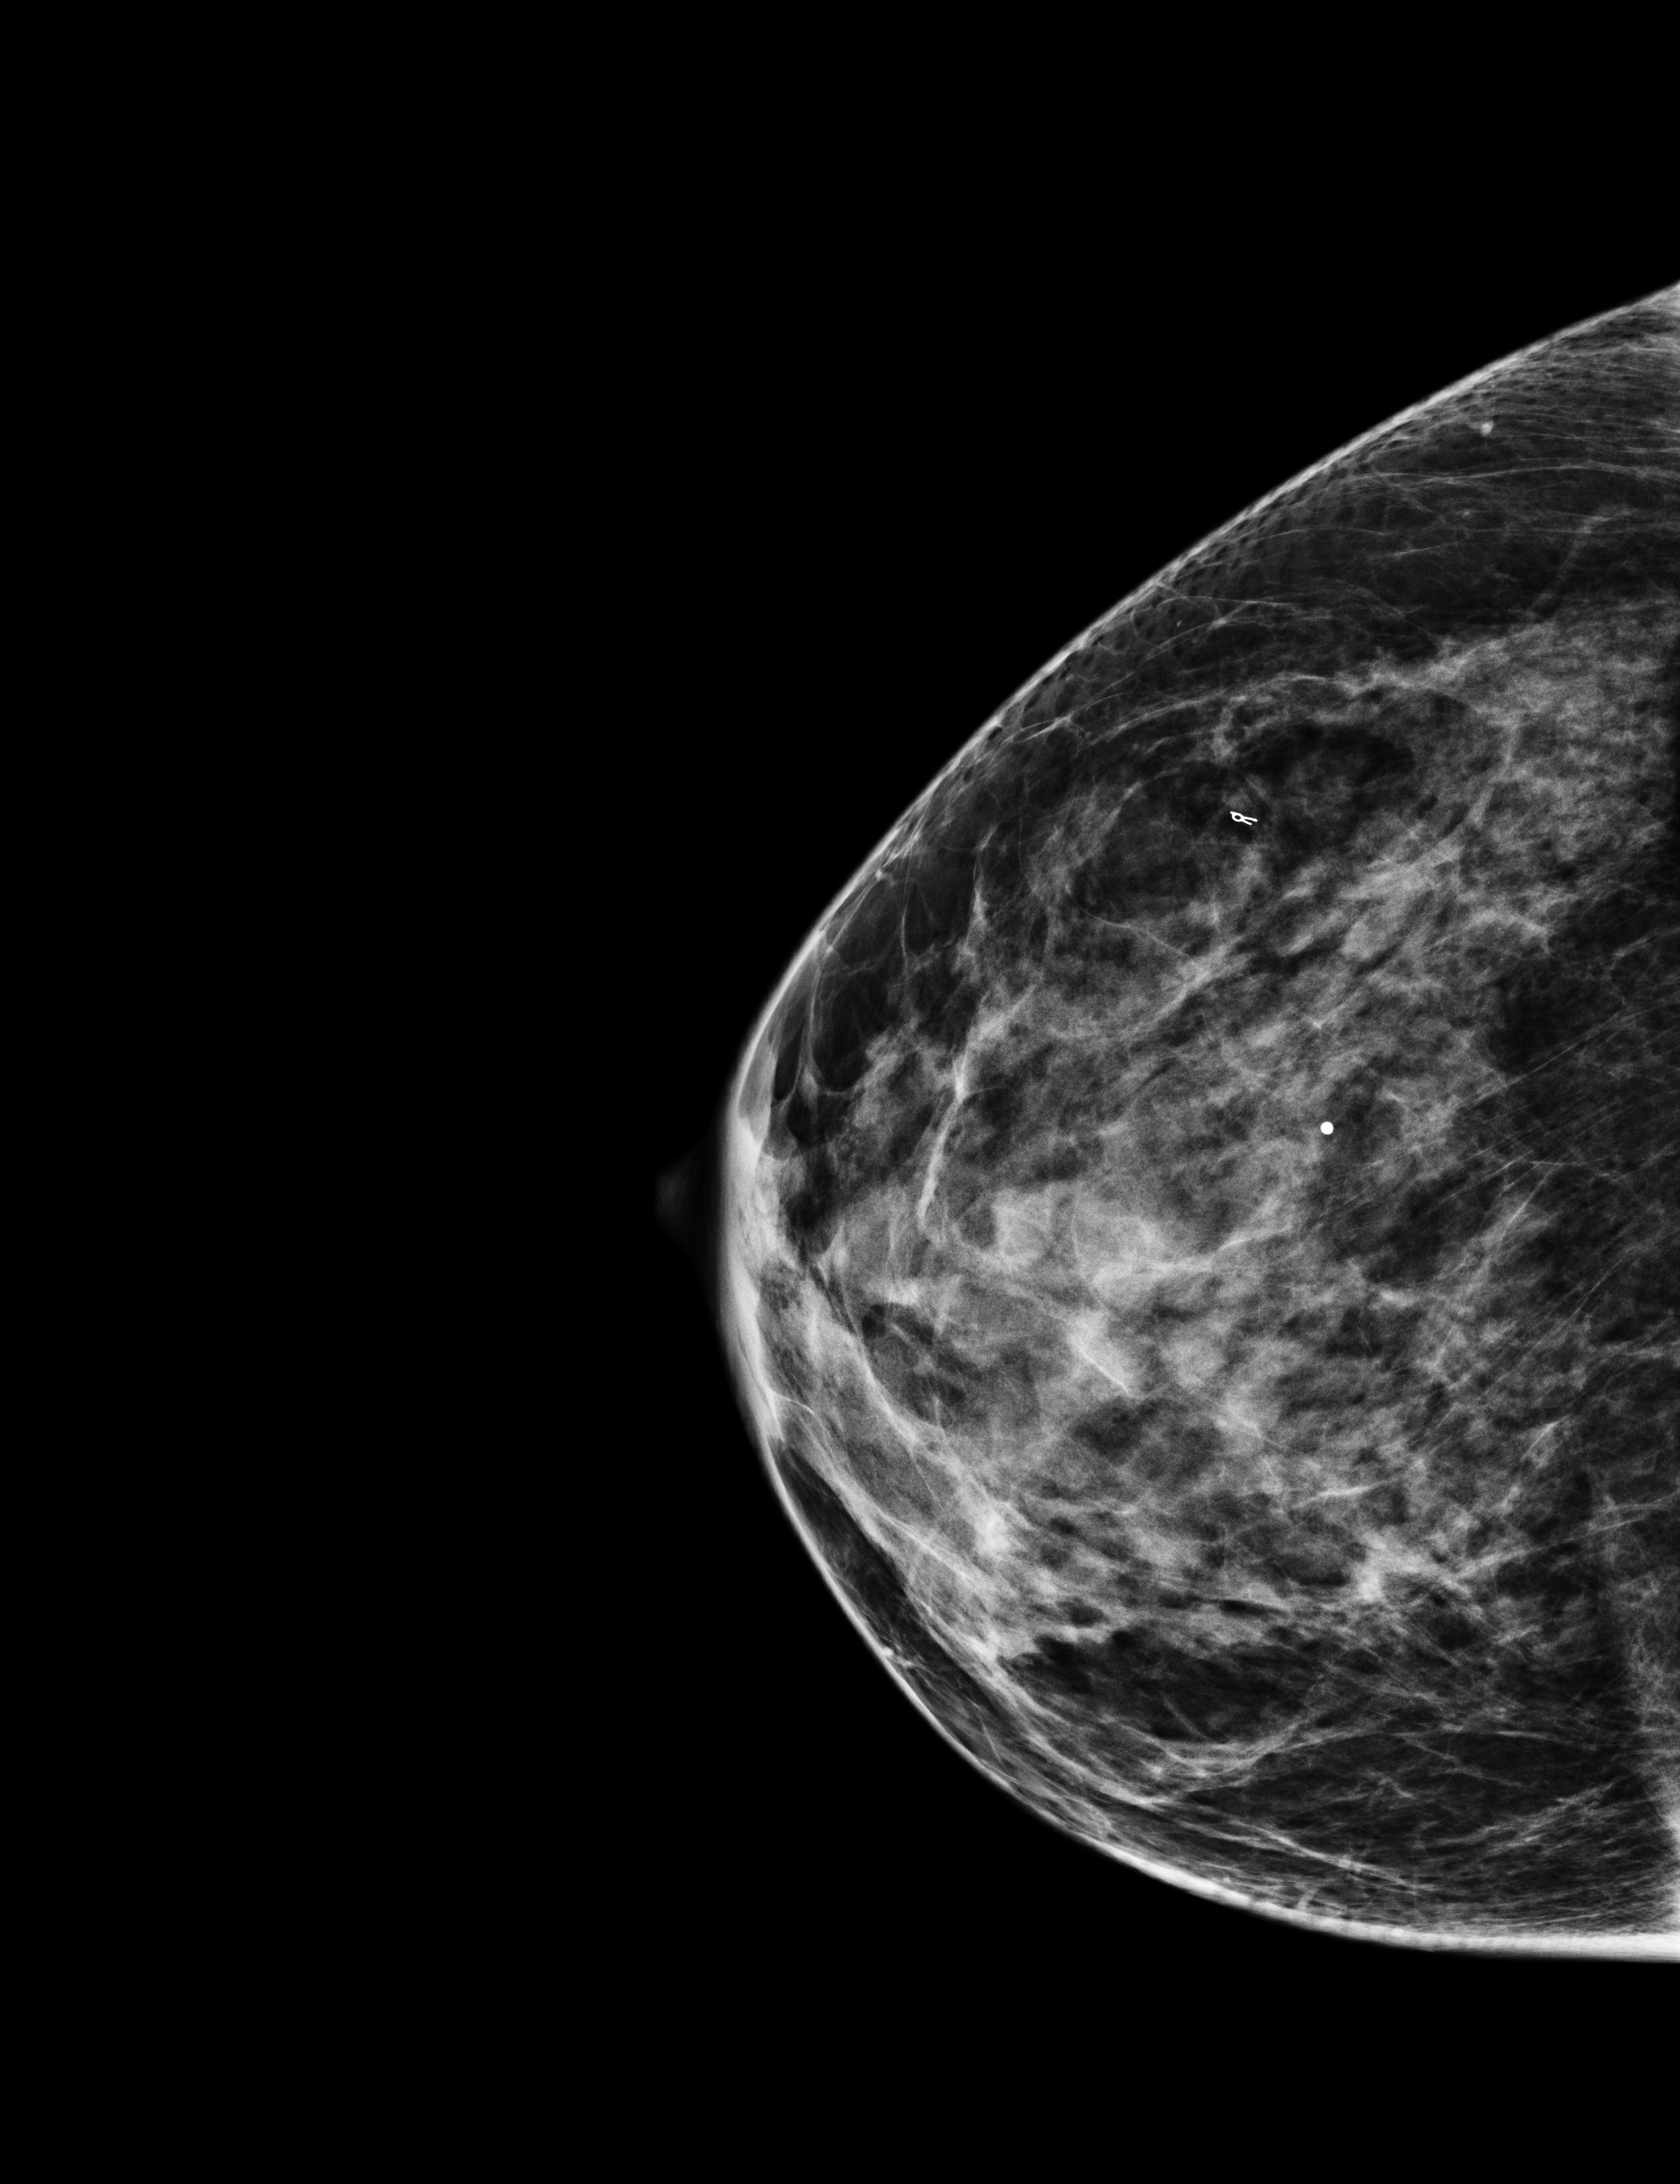
Full-field digital mammogram (FFDM); right breast; craniocaudal (CC) view; screening examination; compressed breast thickness 45 mm. Patient: female, 62 years.
BI-RADS breast density category at the screening exam (both breasts, scale 1–4): 3. Final BI-RADS assessment for this screening round (tomosynthesis exam, both breasts): category 2. Recall: no recall after this screen.